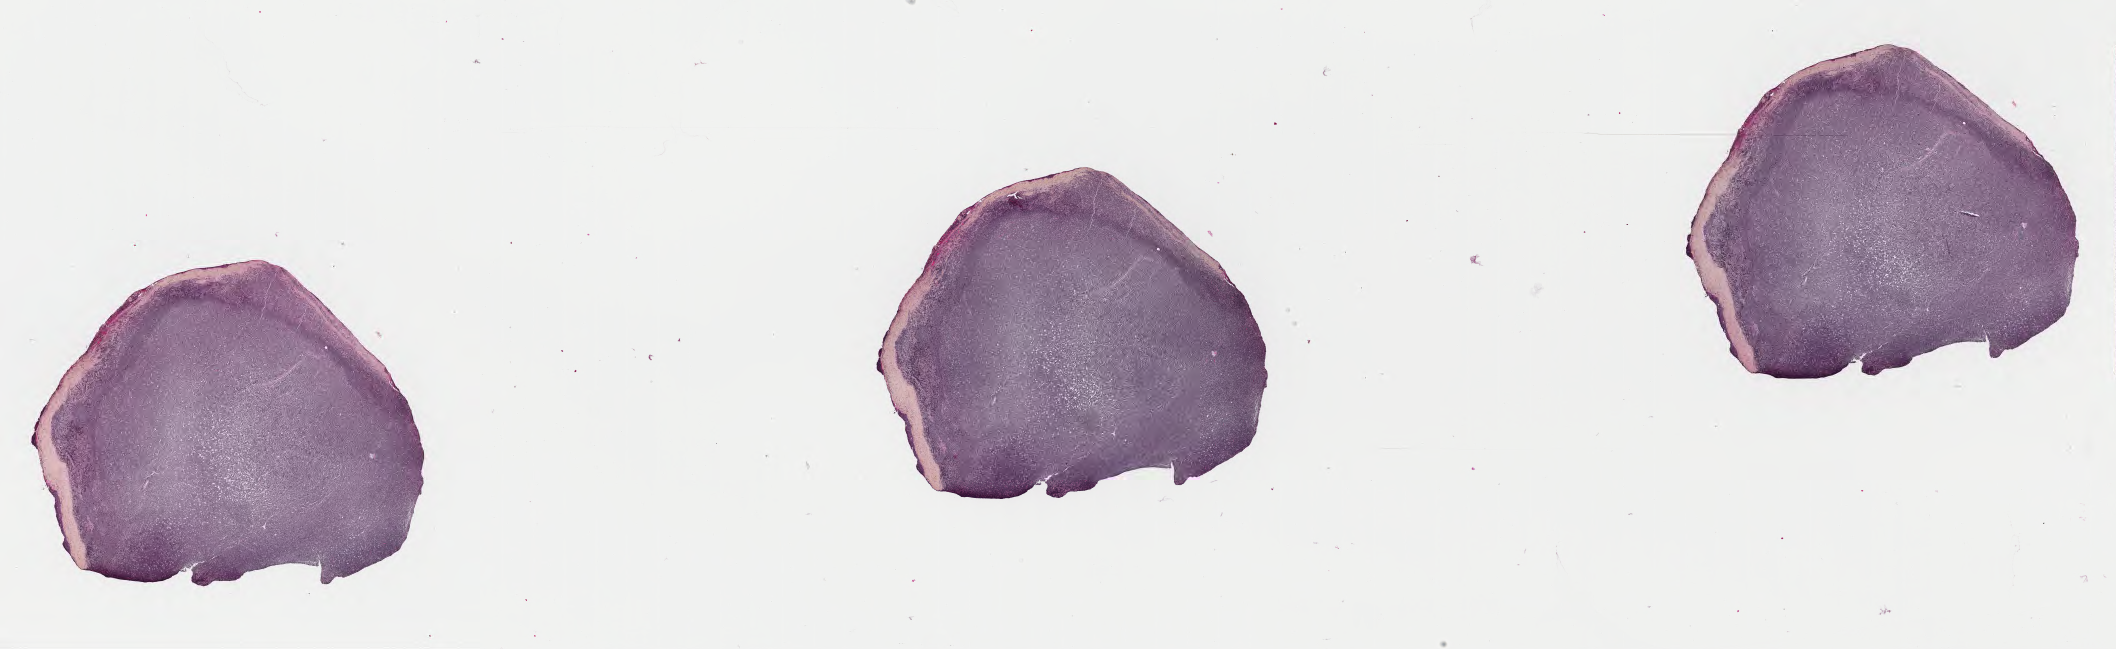
Digitized haematoxylin and eosin-stained section — a low-resolution overview of the entire scanned area, about 34.2 x 10.5 mm; formalin-fixed paraffin-embedded section; specimen: primary tumor. Patient male; 45 years old. Slide review estimates, as recorded: tumor cells 90%, tumor nuclei 95%, stromal cells 10%, necrosis 0%, normal cells 0%. Inflammatory infiltration, as recorded: lymphocyte infiltration 20%, monocyte infiltration 50%, neutrophil infiltration 10%.
* Ann Arbor stage (patient): Stage IV
* diagnosis: Burkitt lymphoma, NOS